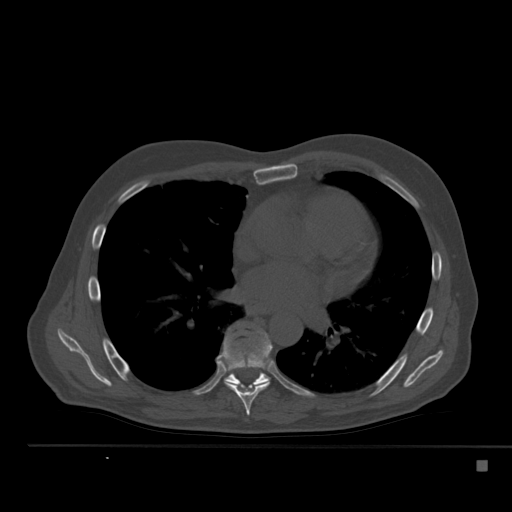
CT including the spine, one axial slice. Slice 320 of 517 in the series (ordered by position). Reconstruction kernel Br40s. 120 kVp. Bone window (W 1800 / L 400 HU). 1.5 mm slice thickness. 512 × 512 image matrix. Male patient, age 70 years. From the clinical record (not read from this slice): primary cancer: renal.
Structures marked on this image (semi-automatic segmentation, software-assisted and operator-edited):
- T7 vertebra: bounding box [x1, y1, x2, y2] px = [222, 333, 272, 416]
- T8 vertebra: [224, 334, 270, 390]